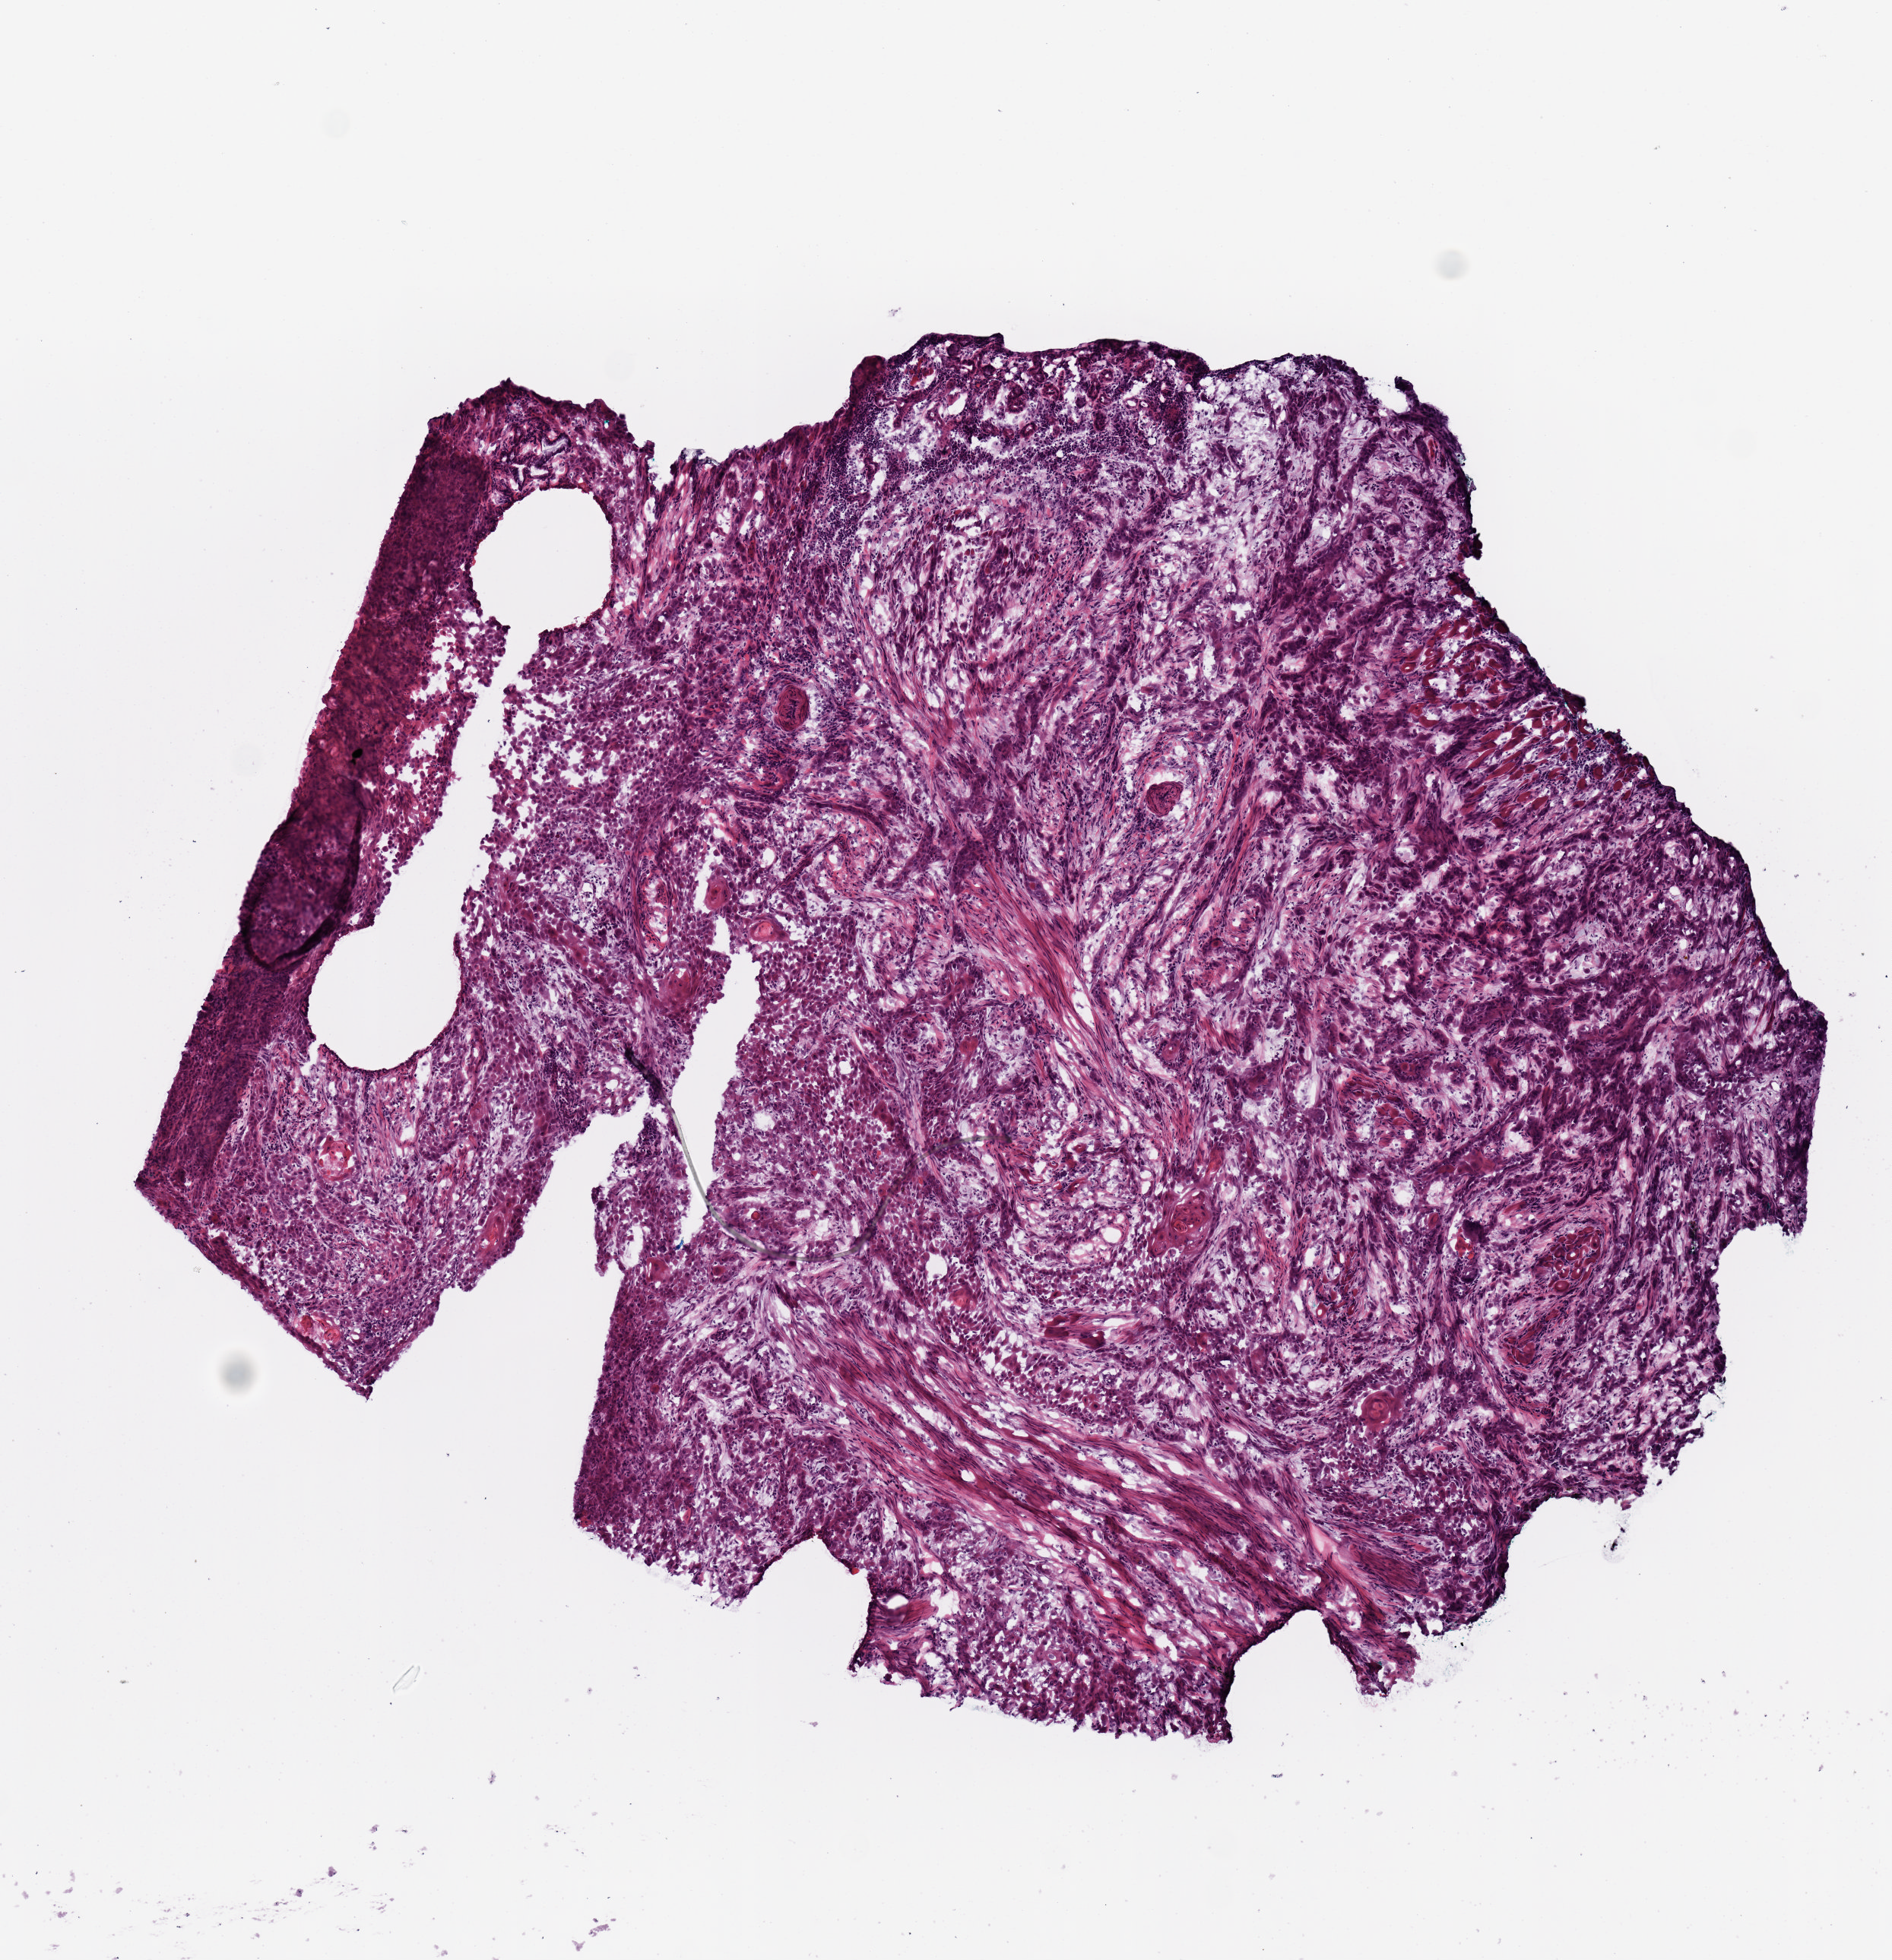
Whole-slide histology image, Hematoxylin and eosin (H&E) stained — shown as a low-resolution overview of the whole scanned area (about 4.9 x 5.1 mm, from a 20x scan), frozen section, sample: primary tumour, head and neck. Female, age 61 years at initial diagnosis. Histologic grade: G2 (moderately differentiated). Pathologist review of this section (percent, as recorded): tumour cells 100%, tumour nuclei 65%, normal cells 0%, stromal cells 0%, necrosis 0%. Infiltration values recorded for this section: lymphocyte infiltration 25%, monocyte infiltration 0%, neutrophil infiltration 5%.
- AJCC pathologic stage: III (7th edition)
- lymph nodes positive (case pathology): 1 of 1 examined
- diagnosis: Squamous cell carcinoma, NOS (tongue, NOS)